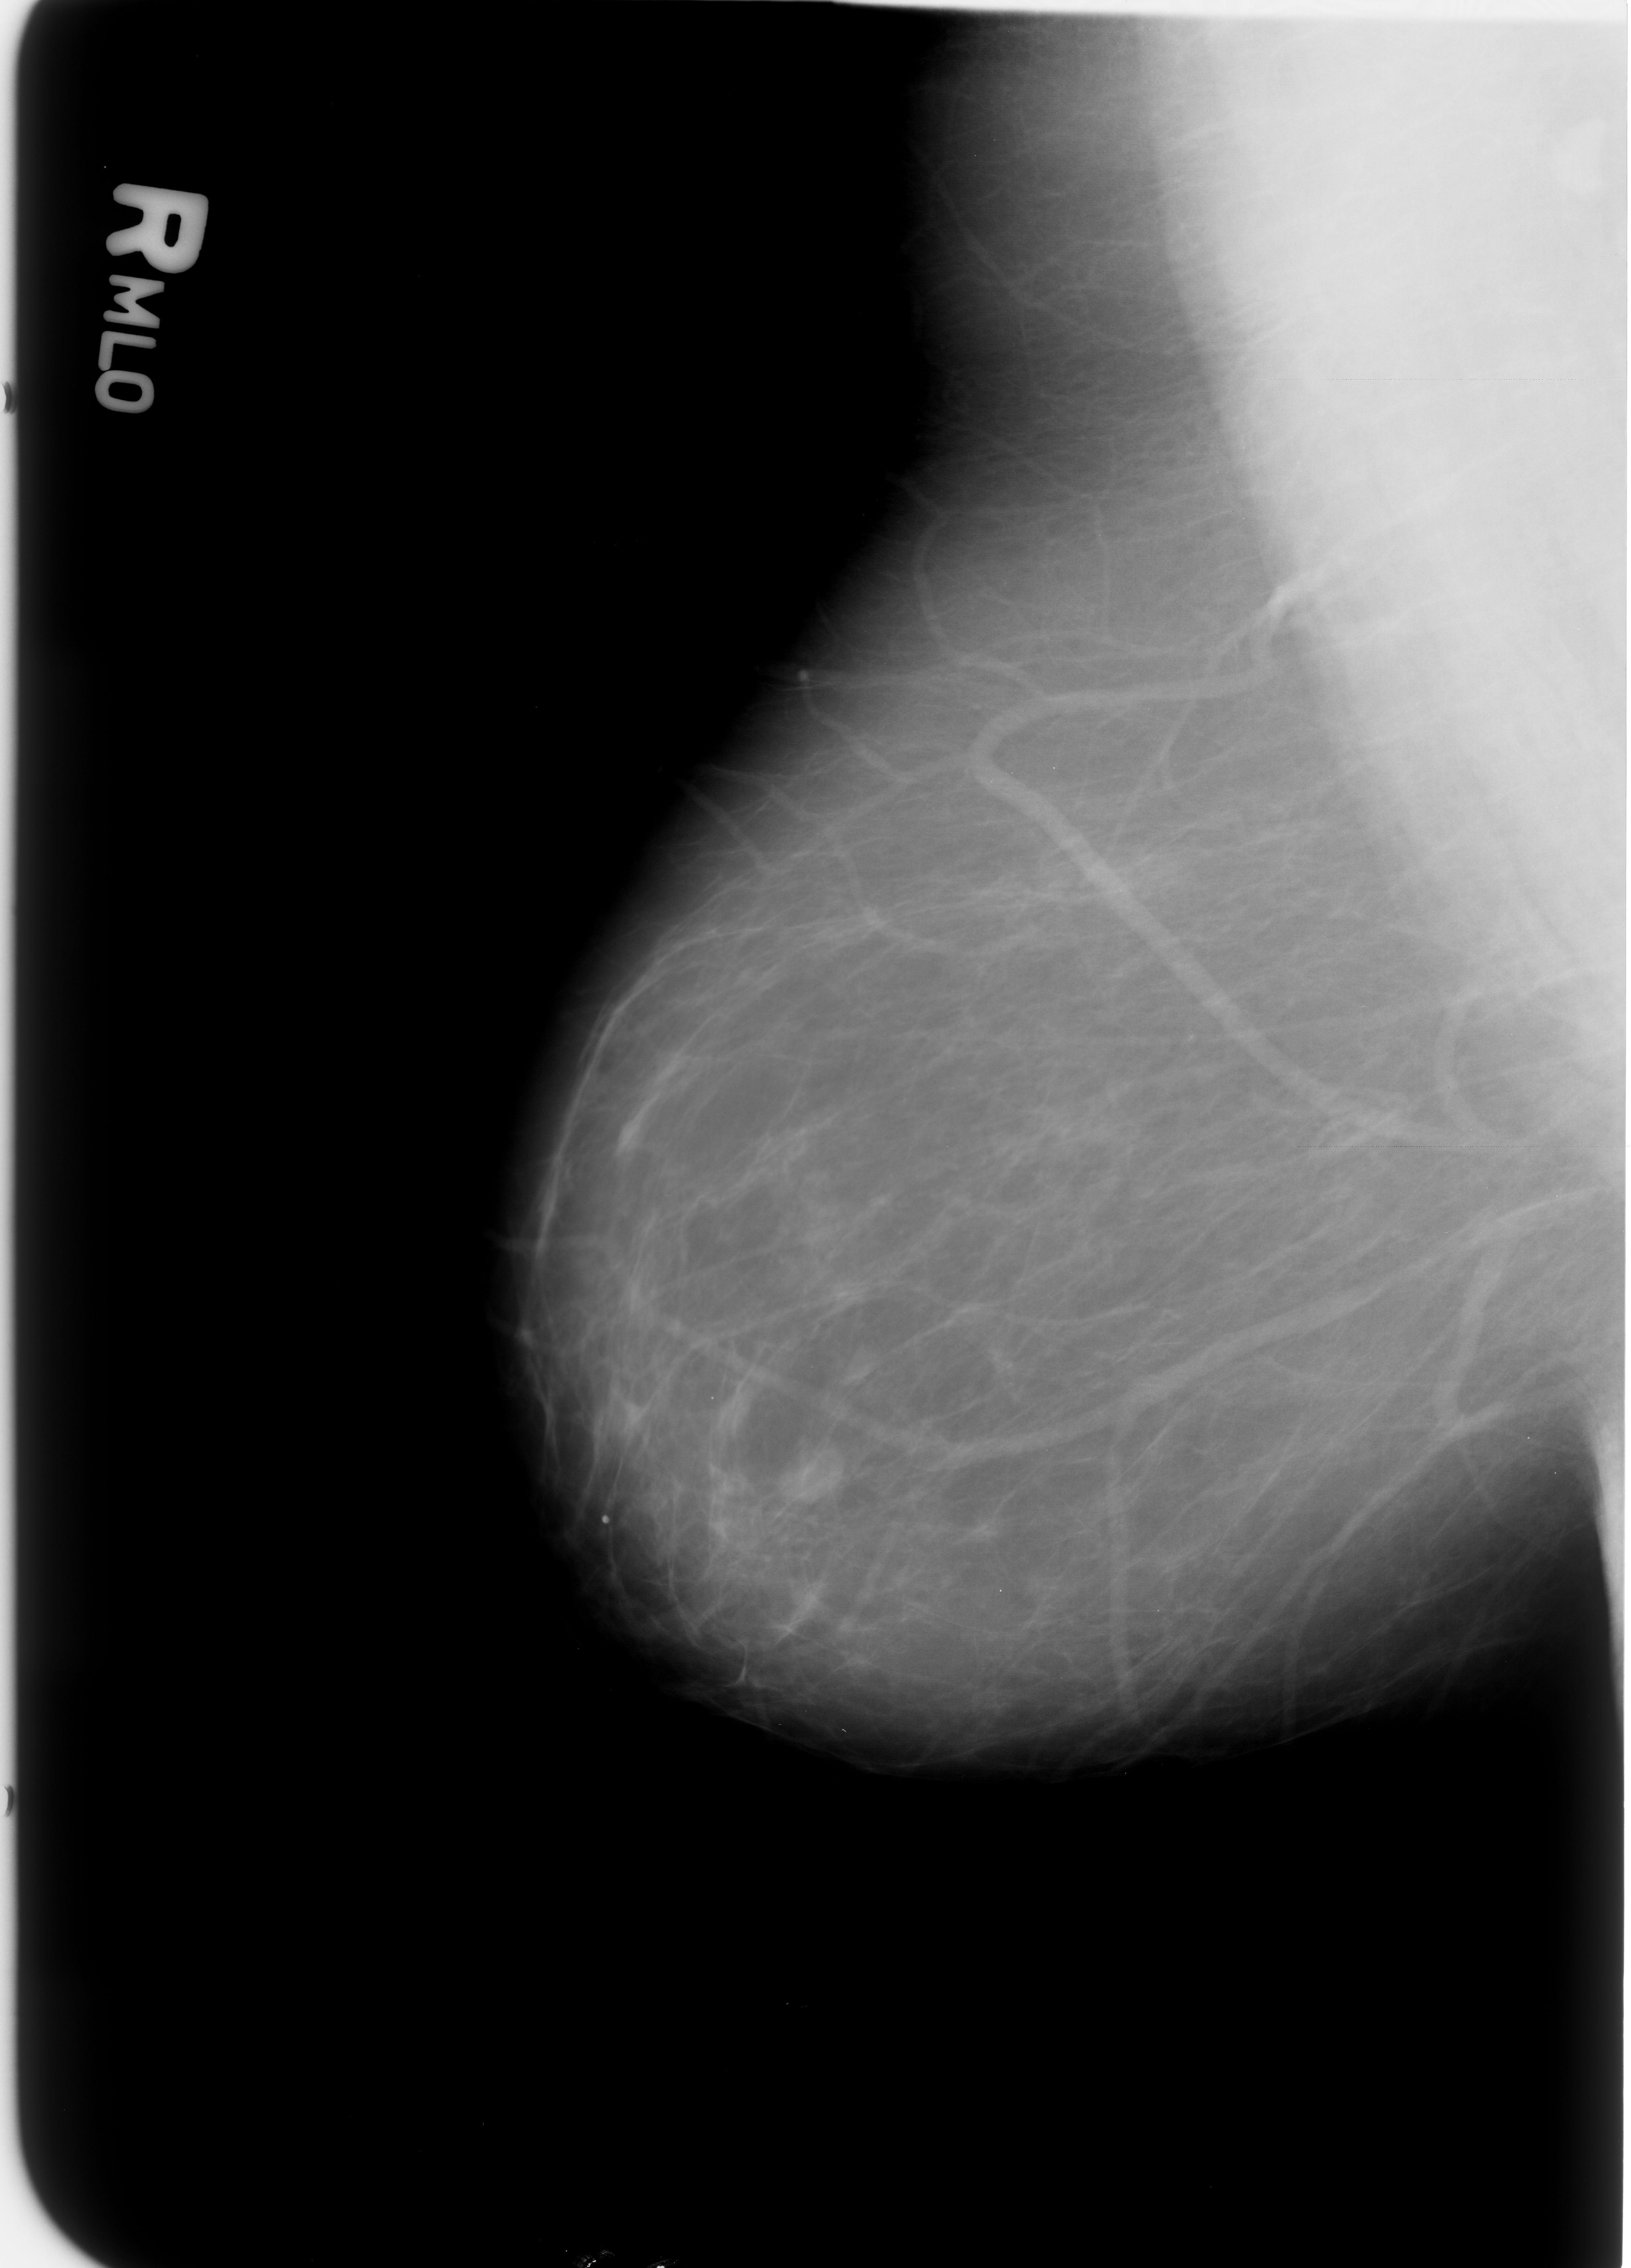
Scanned film-screen mammogram; right breast; mediolateral oblique (MLO) view; breast composition: almost entirely fatty (BI-RADS density category 1 of 4); 1631 × 2268 image matrix.
Marked abnormalities (boxes around the expert regions of interest):
- mass, shape lobulated, margins circumscribed / ill defined; BI-RADS assessment category 4; subtlety rating 3 on a 1 (subtle) to 5 (obvious) scale; pathology (as recorded): benign: box from (x=773, y=1435) to (x=851, y=1505) px